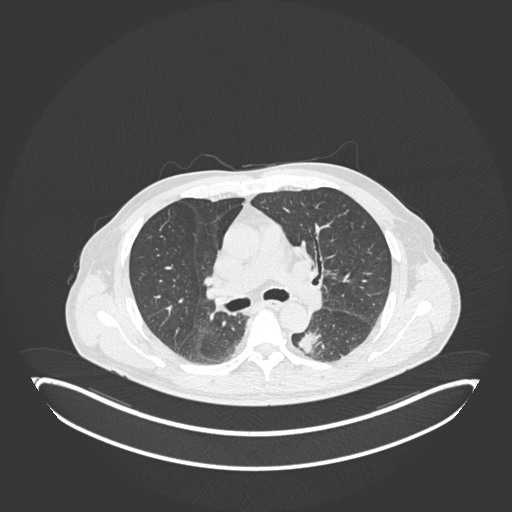
Chest CT, one axial slice. Position 129 of 251 along the scan axis. Reconstruction kernel B30f. 120 kVp. Lung window (W 1500 / L -600 HU). 1 mm slice thickness. 512 × 512 image matrix, field of view 500 × 500 mm. Patient: male, 72 years. Case-level facts recorded for this patient, not image findings: clinical TNM (as recorded): T2b N0 M1.
Outlined on this slice (rectangle marked by the reading radiologist):
- lung tumour (recorded histology: adenocarcinoma): bounding box [x1, y1, x2, y2] px = [294, 328, 325, 358]